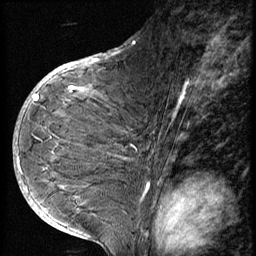
Breast MRI (dynamic contrast-enhanced), one sagittal slice. Position 34 of 56 along the scan axis. 3 images stored at this slice position (order not interpretable as contrast timing). 1.5 T. TE 4.2 ms, TR 9 ms. 256 × 256 image matrix, field of view 180 × 180 mm. Female patient, age 49 years. Case-level facts recorded for this patient, not image findings: setting: breast cancer imaged before/during neoadjuvant chemotherapy; receptor status: HER2-positive.
Structures marked on this image (semi-automatically segmented with operator editing):
- analysis volume of interest (the breast-tissue region the enhancement analysis was run in; not a lesion): bounding box <37,85,129,207> (left, top, right, bottom; pixels)
- tumour enhancement mask (voxels above the 140 % enhancement threshold inside the analysis volume of interest): <37,86,83,101>